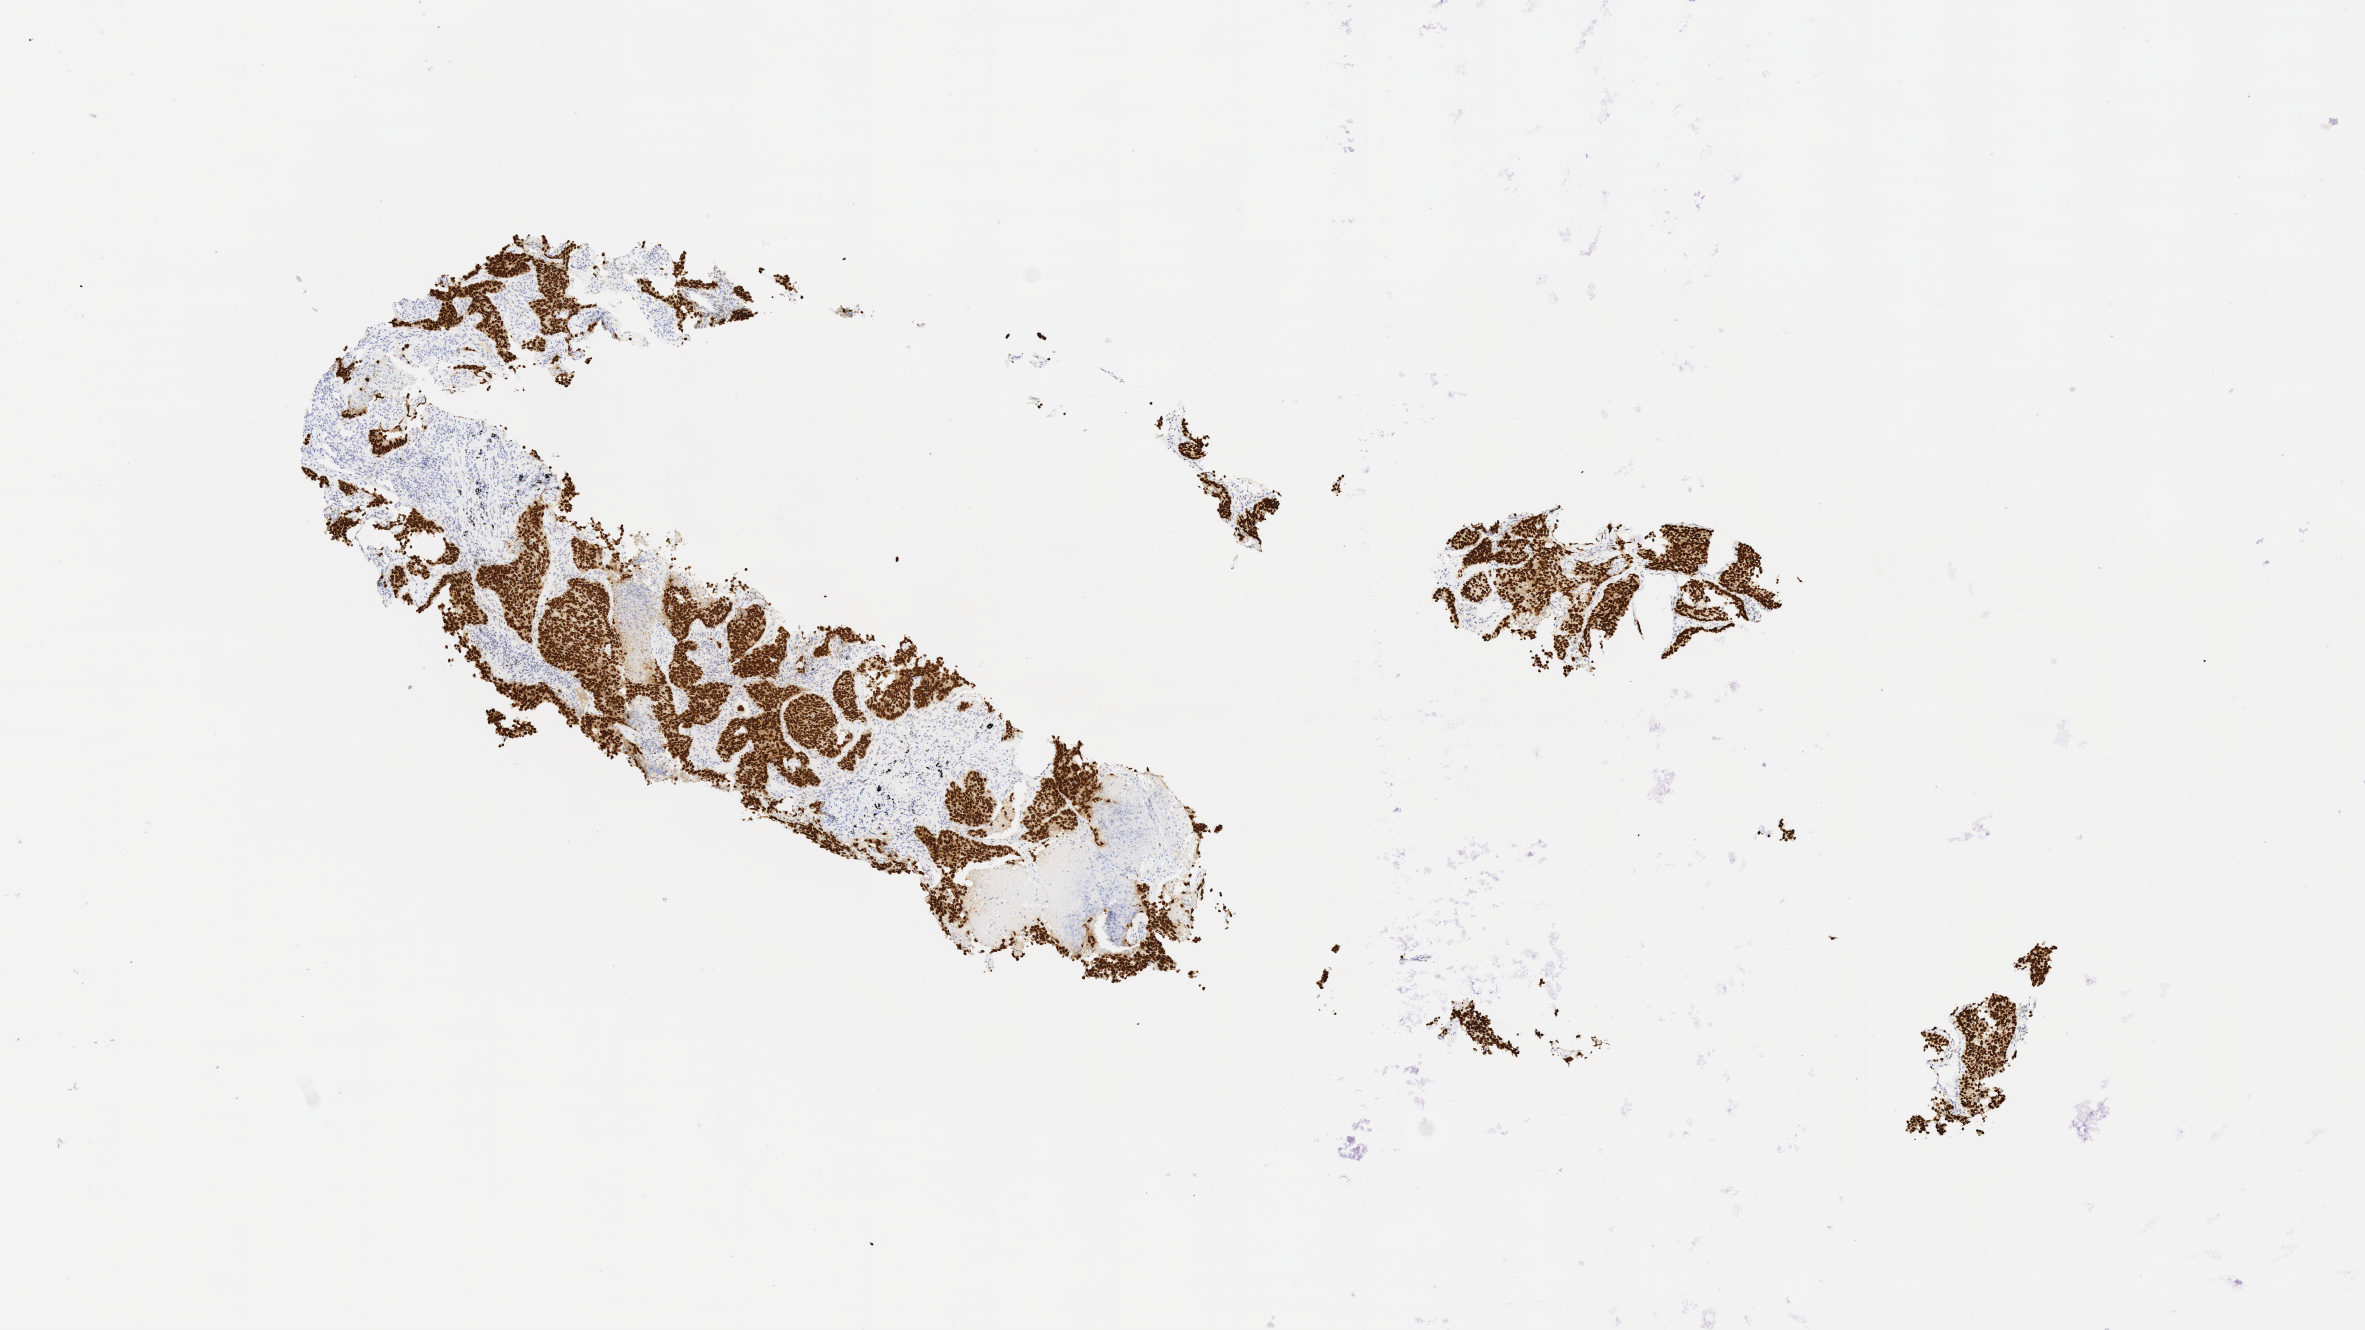
Whole-slide image, immunohistochemical stain for TTF-1 (thyroid transcription factor 1), whole scanned area (about 9.6 x 5.4 mm) shown as a low-resolution overview. Specimen: tumor tissue. Site: lung. Patient: male, age 68 years.
Histologic diagnosis: Bronchiolo-alveolar carcinoma, non-mucinous.